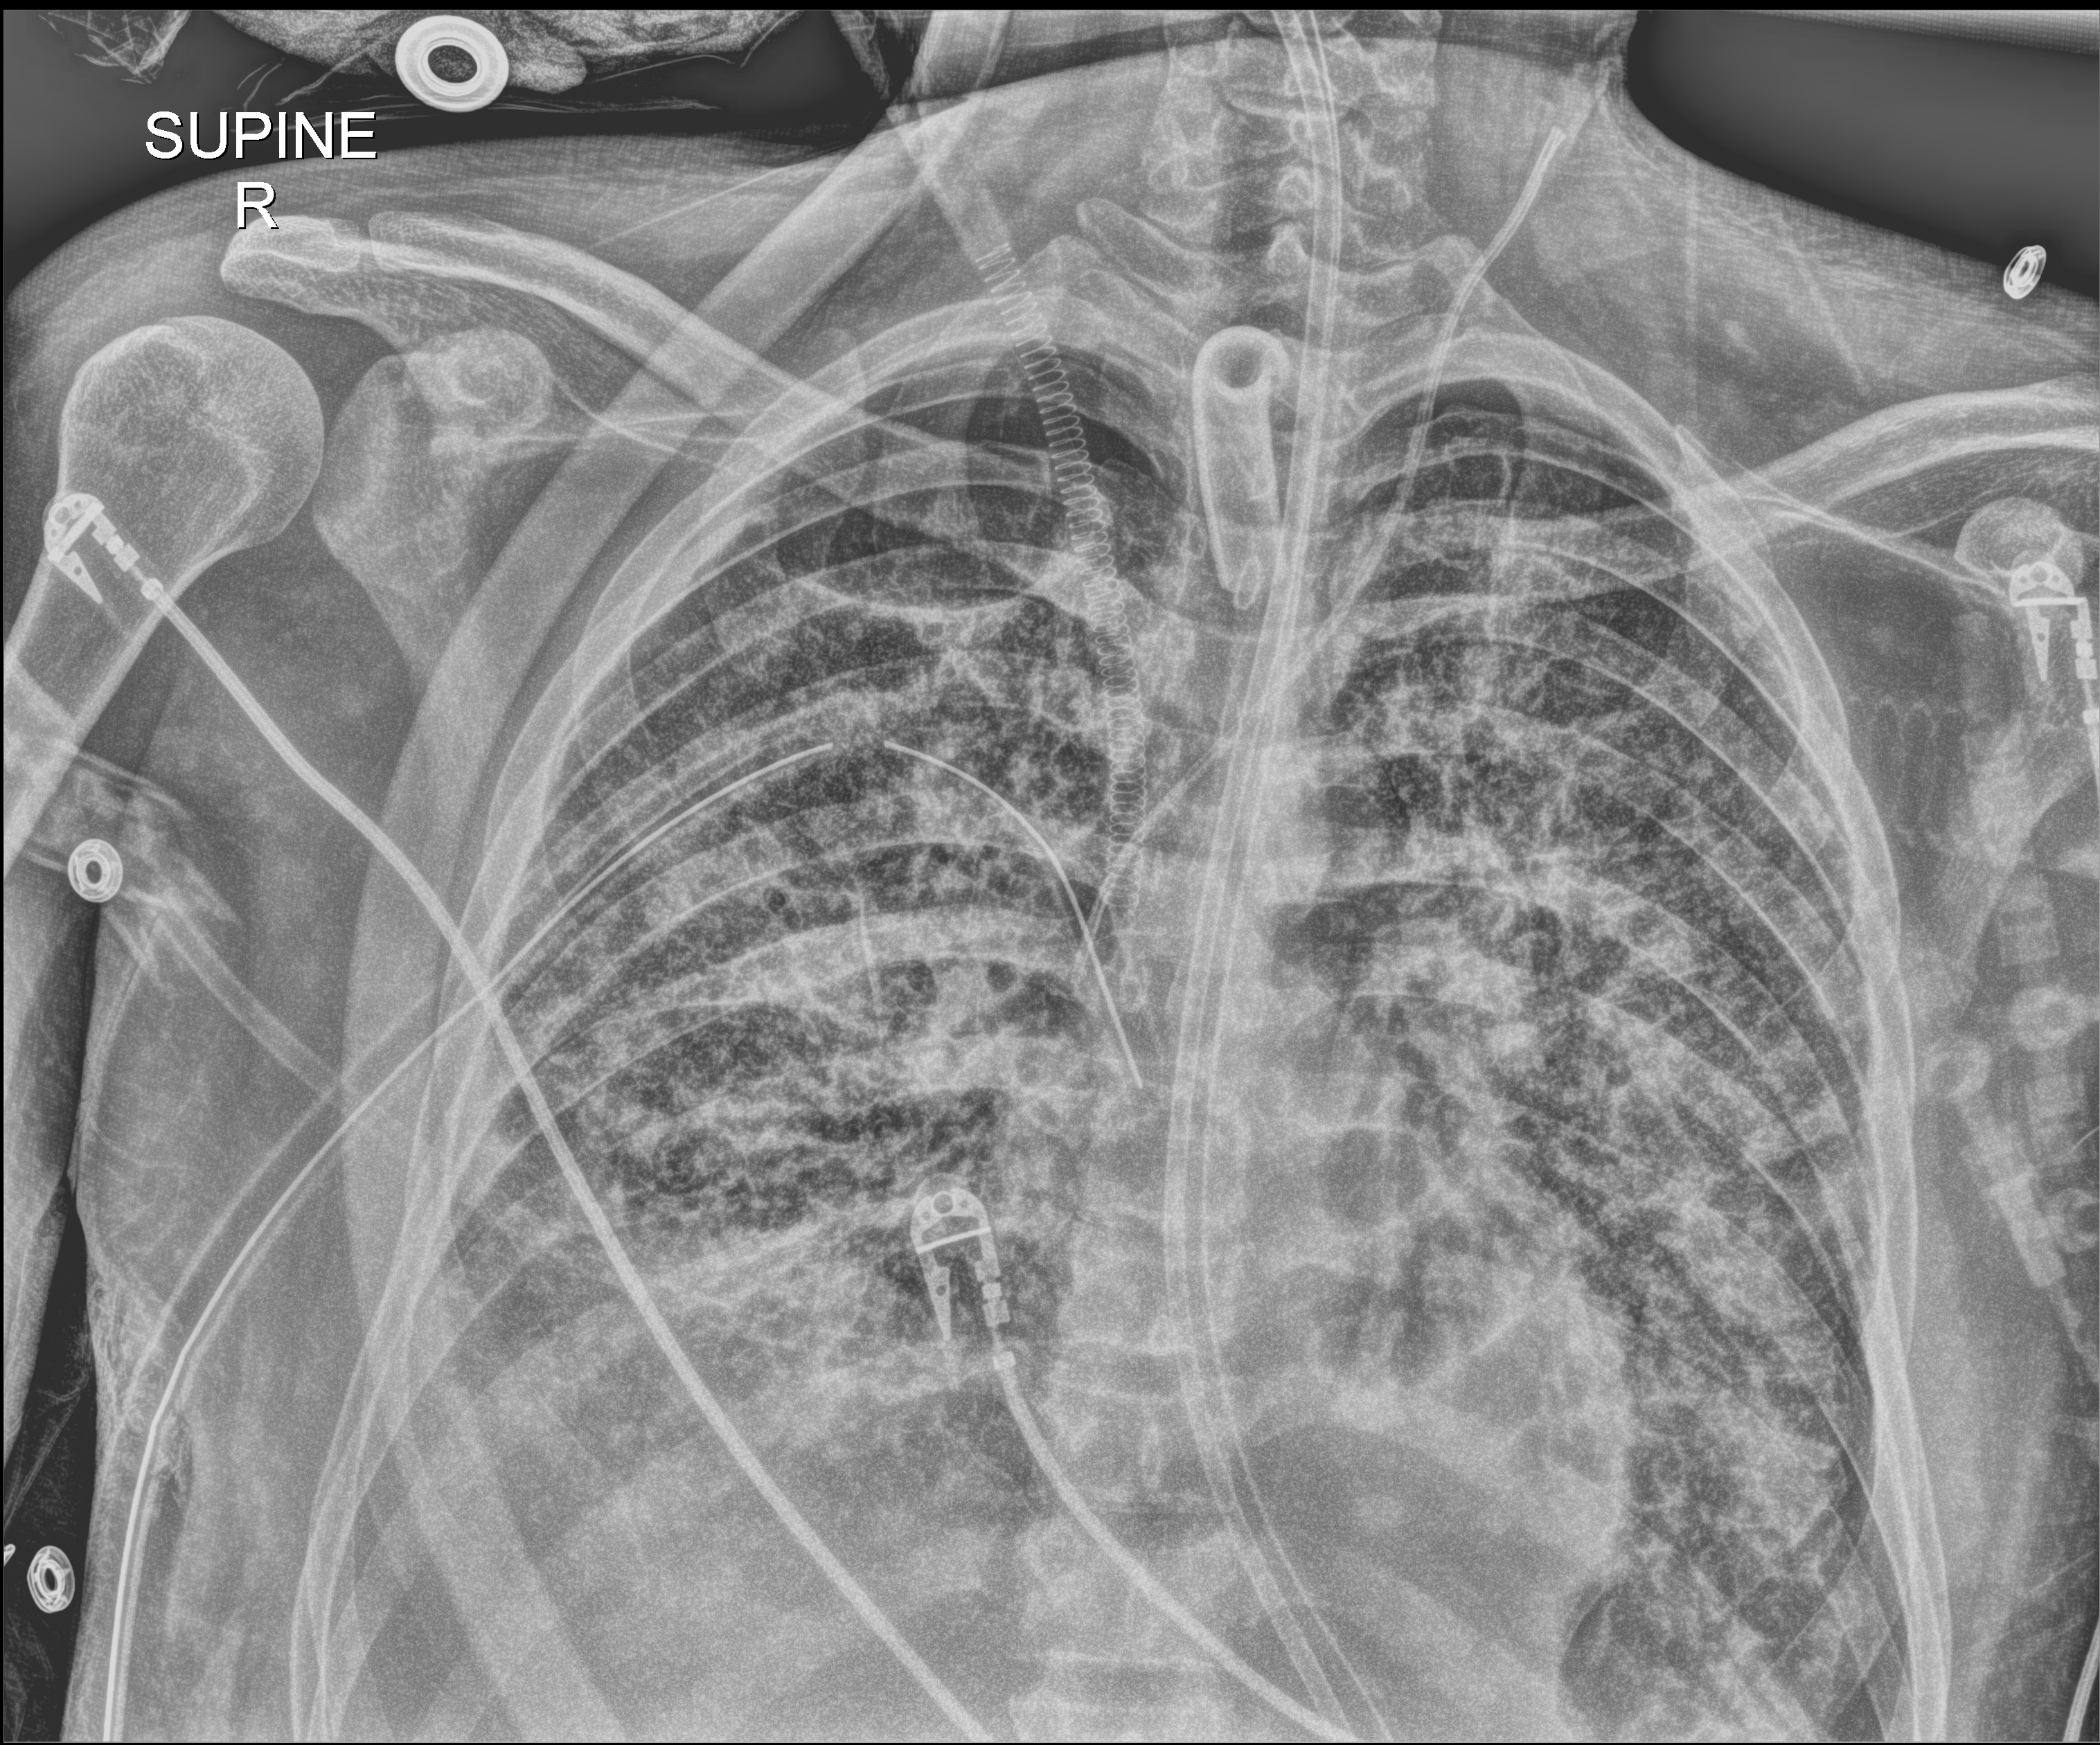
Chest X-ray. Patient hospitalised with COVID-19, aged 18–59 years.
From the hospital-stay record, not from the radiograph (when in the stay this image was taken is not recorded): admitted to intensive care during this hospital stay: yes; other chronic lung disease (admission record): no; mechanically ventilated during this hospital stay: yes.